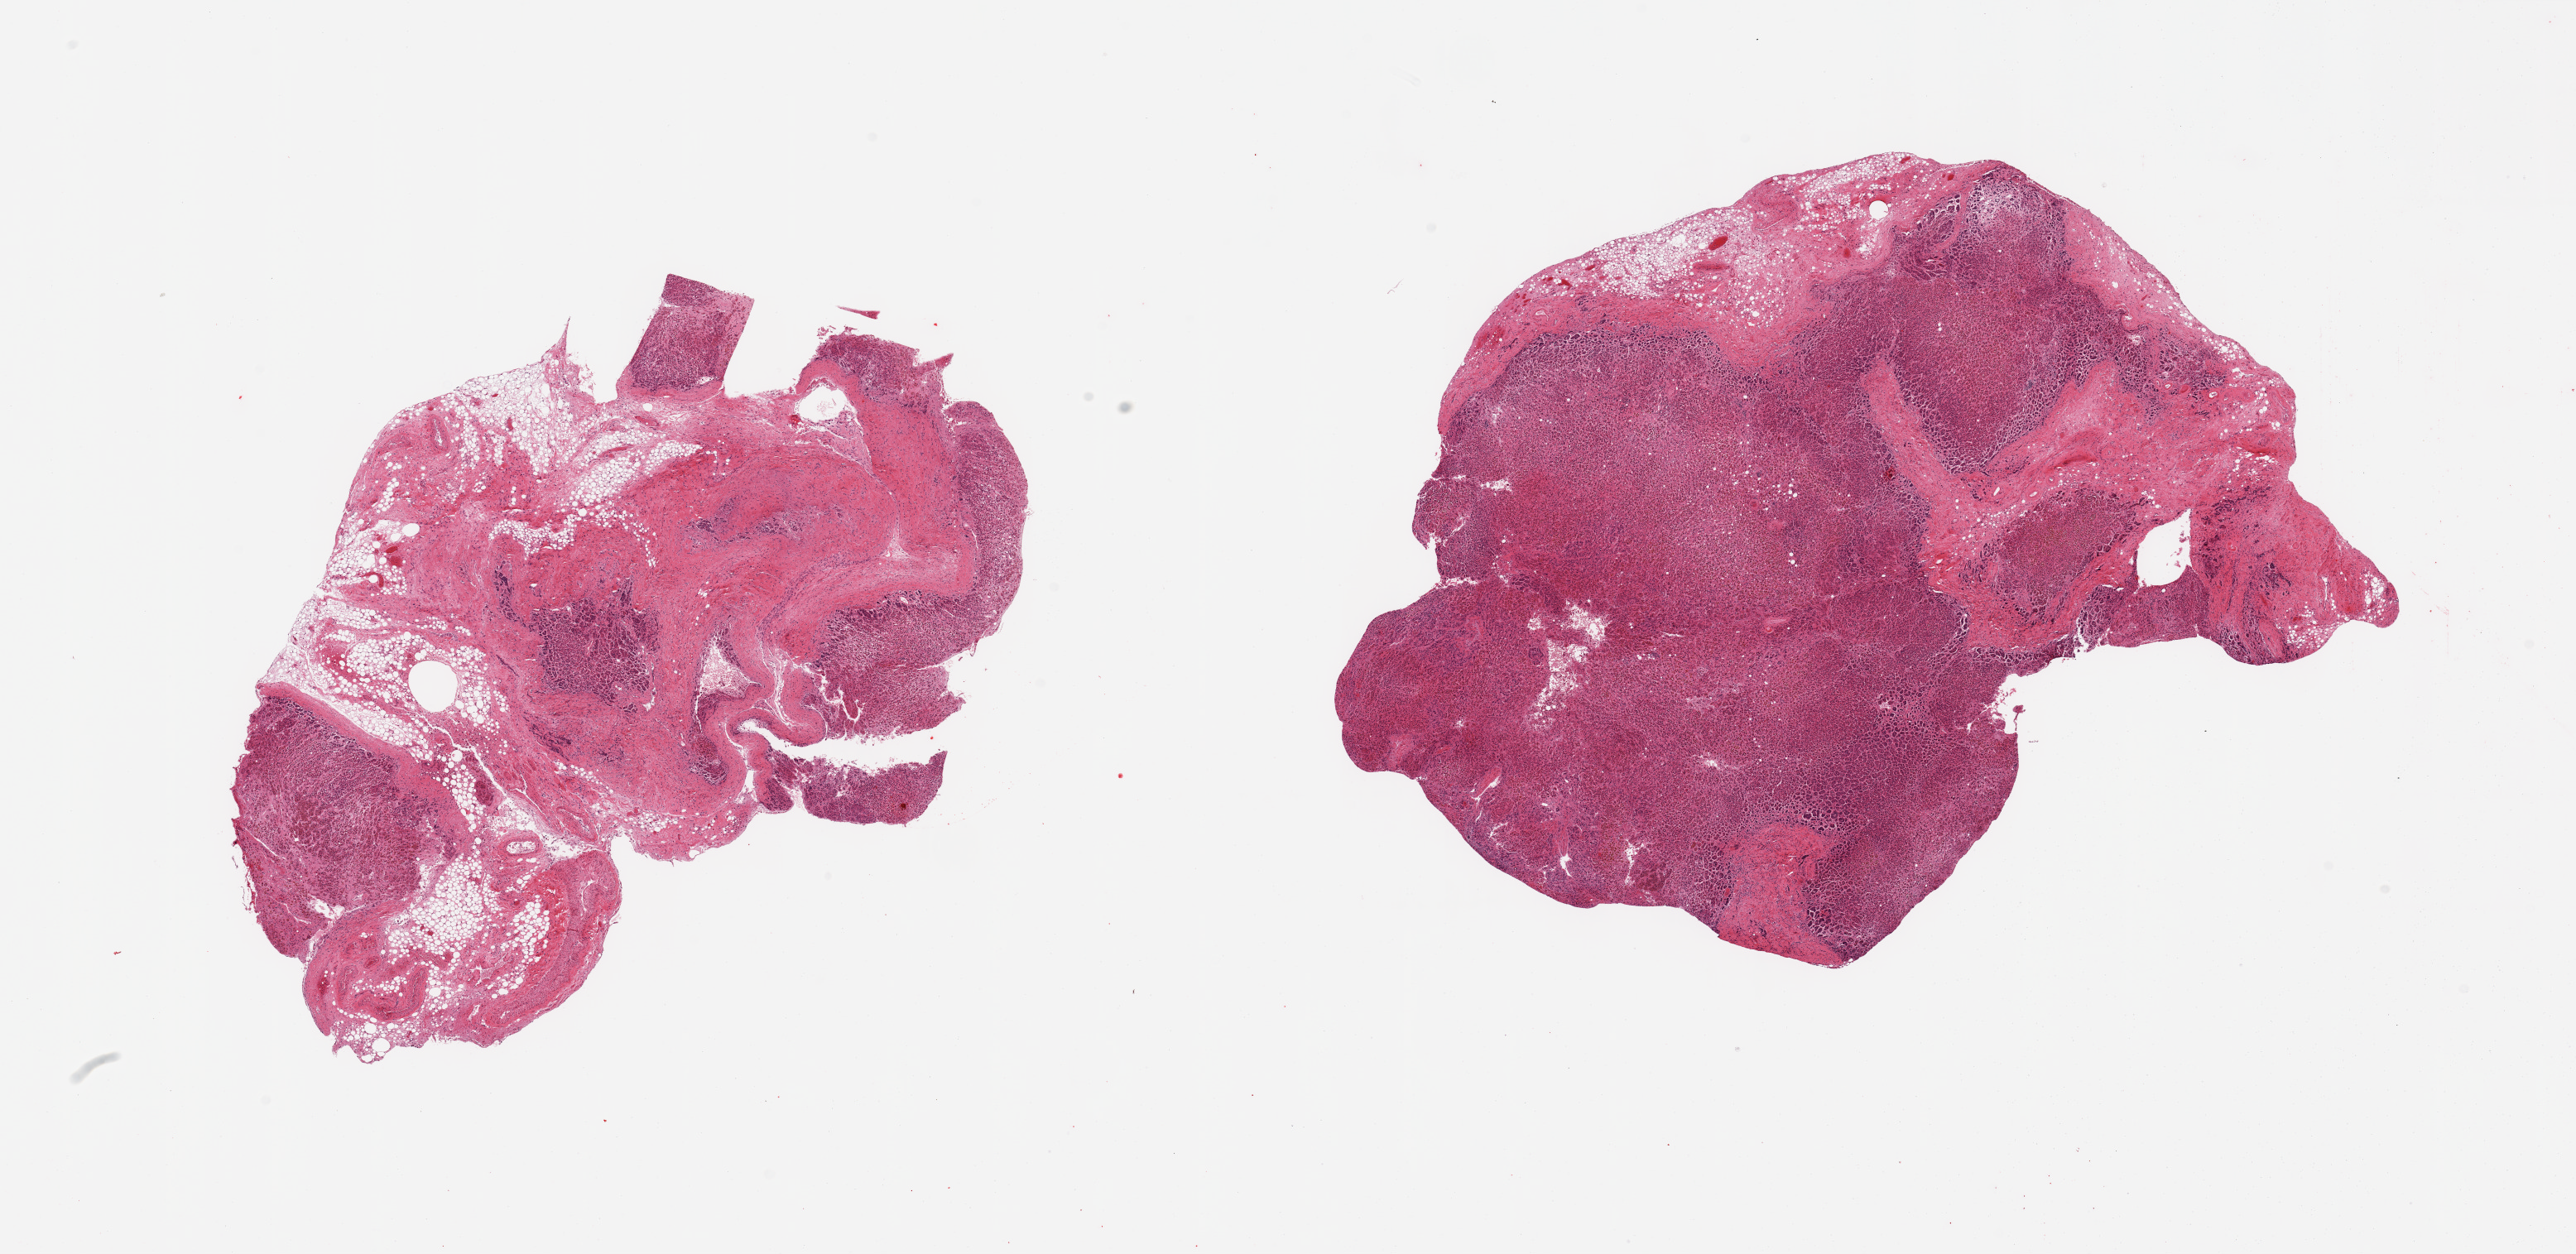
Haematoxylin and eosin whole-slide image, brightfield, a low-resolution overview of the entire scanned area, about 24.6 x 12.0 mm (slide scanned at 20x); PAXgene-fixed, paraffin-embedded tissue; target tissue: adrenal gland; tissue donor sample. Donor: female.
• reviewer comment on this tissue sample: 2 pieces: 1 has 60% fibrofatty content; other has 20%